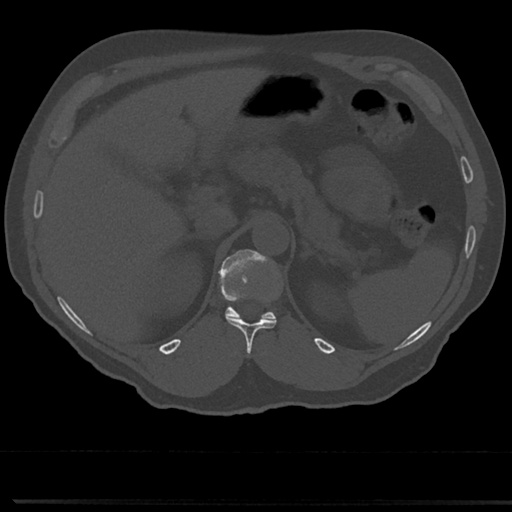
CT including the spine, one axial slice; position 177 of 817 along the scan axis; bone window (W 1800 / L 400 HU); 0.5 mm slice thickness; 512 × 512 image matrix, field of view 355 × 355 mm. Patient: male, 61 years. Case-level facts recorded for this patient, not image findings: primary cancer: prostate.
Annotated regions visible in this slice (semi-automatic segmentation, software-assisted and operator-edited):
- T11 vertebra: bounding box [x1, y1, x2, y2] px = [227, 317, 276, 357]
- T12 vertebra: [217, 250, 279, 321]